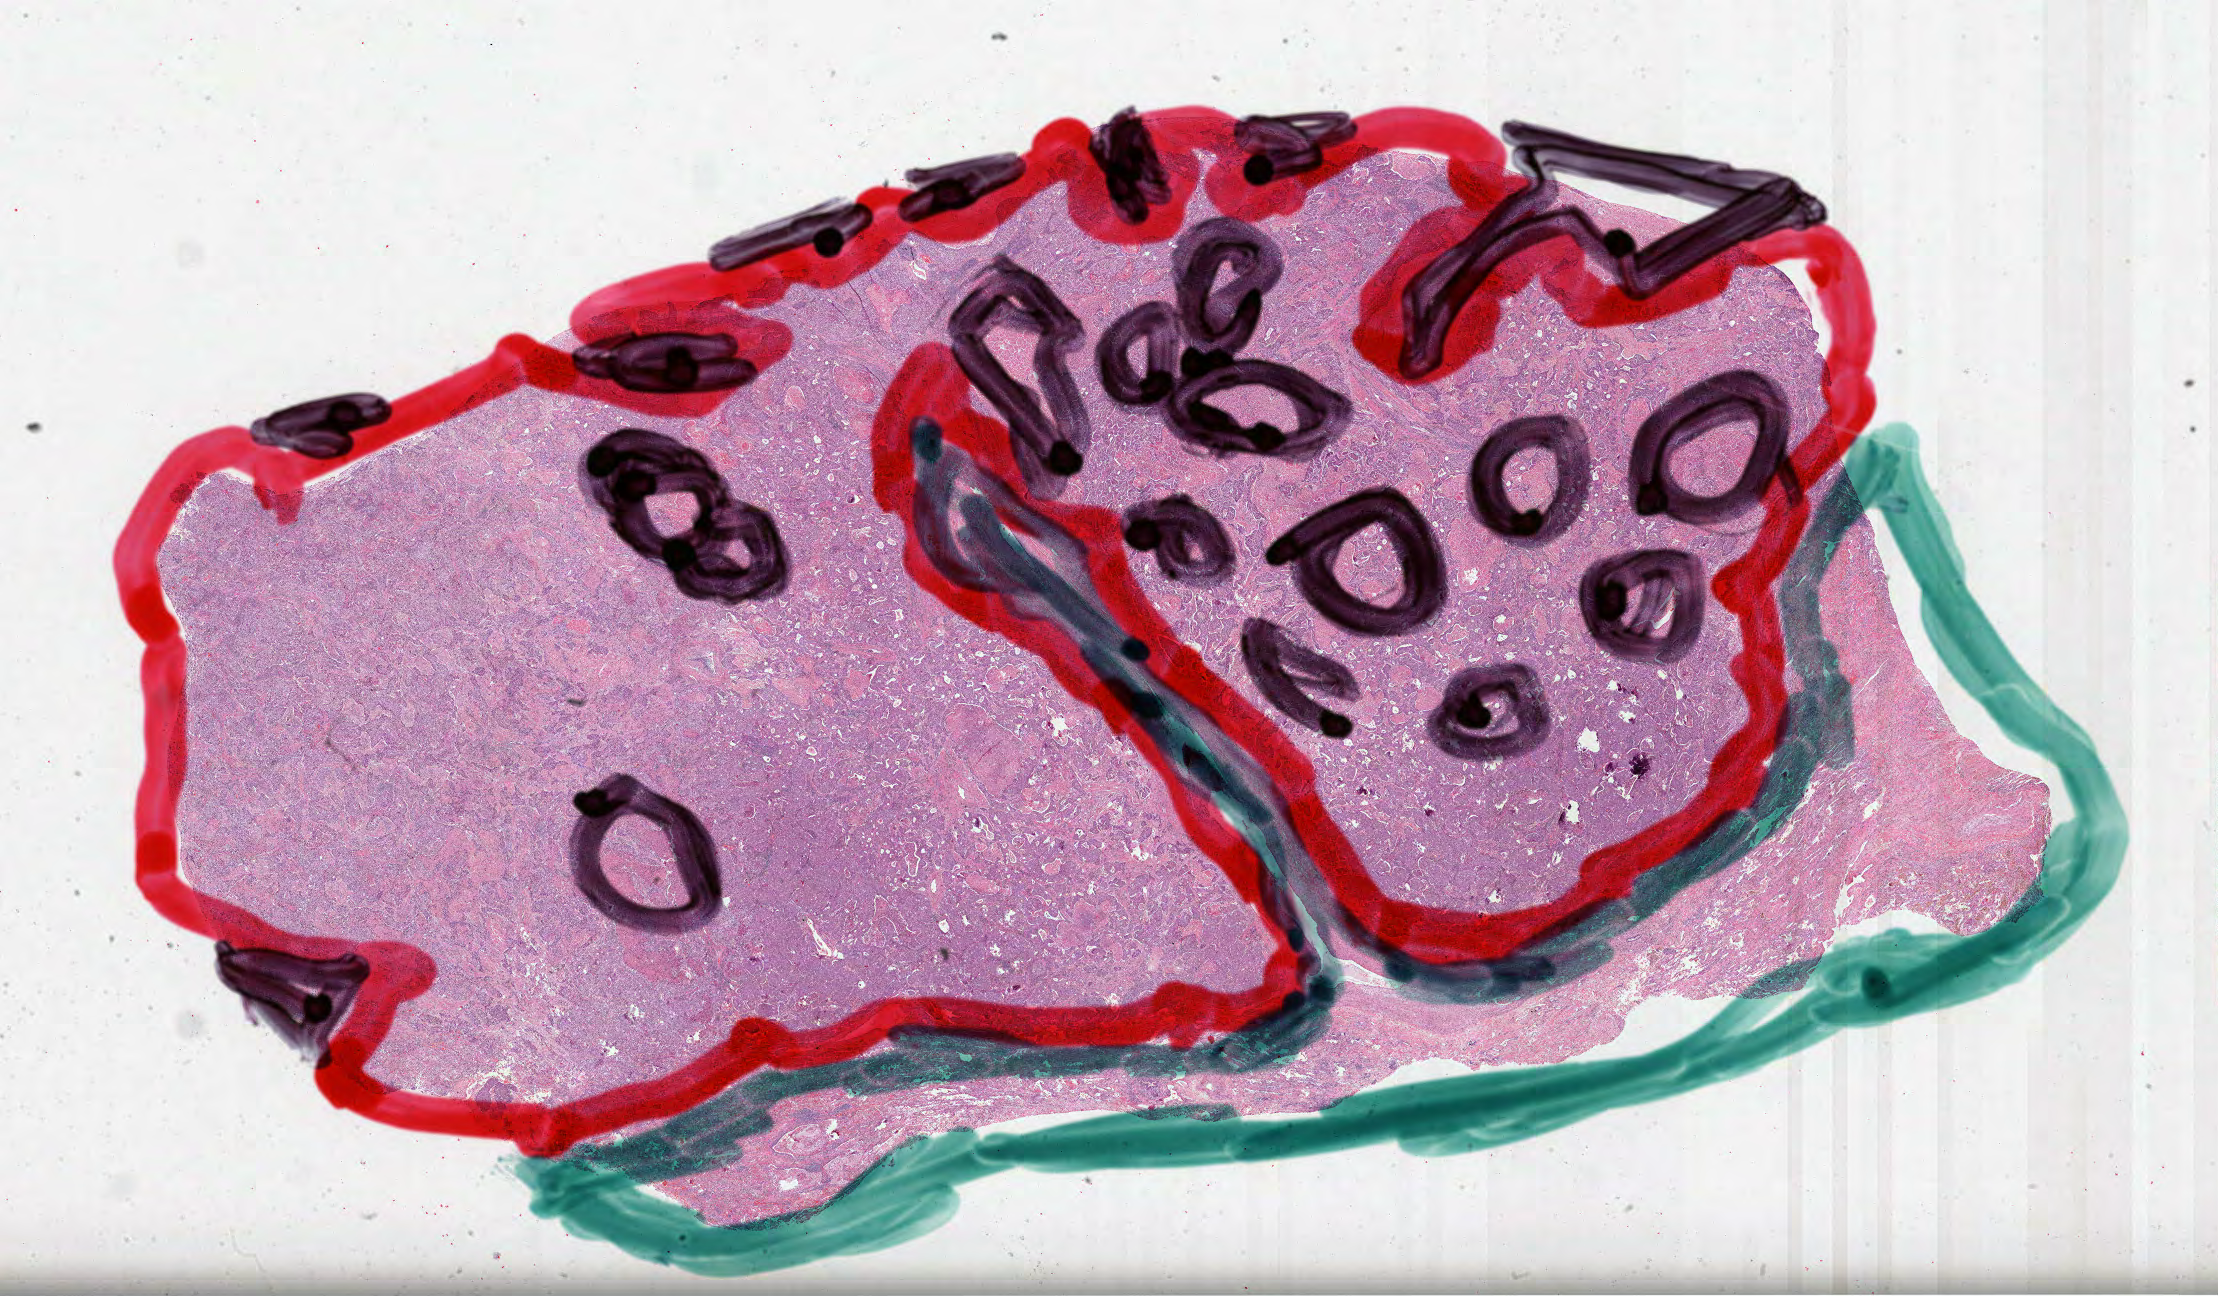
Hematoxylin and eosin (H&E) stained whole-slide image — a low-resolution overview of the entire scanned area, about 35.8 x 20.9 mm. Formalin-fixed paraffin-embedded (FFPE) diagnostic section. Primary tumour sample from the lung. Patient: male, age at initial diagnosis 70 years.
• AJCC pathologic stage: IIIA (7th edition)
• histologic diagnosis: Squamous cell carcinoma, NOS (upper lobe, lung)